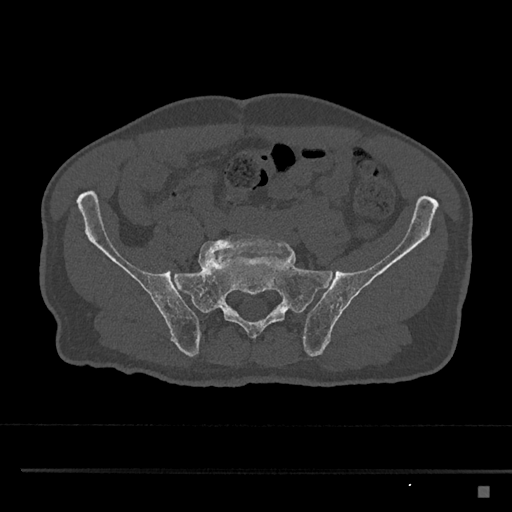
CT including the spine, one axial slice. Slice 535 of 797 in the series (ordered by position). Reconstruction kernel Br40s/3. Bone window (W 1800 / L 400 HU). 0.5 mm slice thickness. 512 × 512 image matrix. Male patient, age 59 years. Case-level facts recorded for this patient, not image findings: primary cancer: prostate.
Structures marked on this image (semi-automatic segmentation, software-assisted and operator-edited):
- L5 vertebra: box from (x=198, y=234) to (x=289, y=269) px